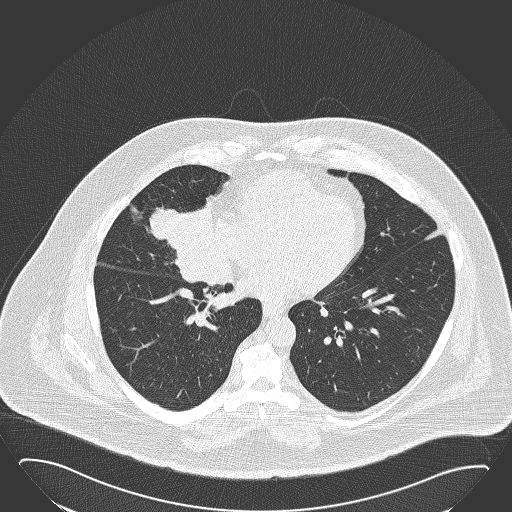
Axial slice from a low-dose chest CT screening exam, baseline annual screen, lung window (W 1500 / L -600 HU), 2 mm slice thickness, slice 97 of 168 in the series. Male, age 61 years at enrolment. Former smoker at enrolment.
Expert reader's lesion annotation, bounding box <140,187,229,275> (left, top, right, bottom; pixels). The screening reader recorded 2 non-calcified nodules or masses ≥4 mm on this exam; which of them this box marks is not recorded. Official screen result: positive, change unspecified: nodule(s) >= 4 mm or enlarging nodule(s), mass(es), or other non-specific abnormalities suspicious for lung cancer.